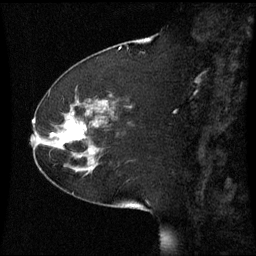
Breast MRI (dynamic contrast-enhanced), one sagittal slice; position 21 of 60 along the scan axis; dynamic contrast-enhanced series, image 2 of 3 at this slice position (ordered by acquisition); 1.5 T; TE 4.2 ms, TR 8.9 ms; 256 × 256 image matrix, field of view 220 × 220 mm. Female patient, age 51 years. From the clinical record (not read from this slice): setting: breast cancer imaged before/during neoadjuvant chemotherapy; receptor status: HR-positive, HER2-negative.
Outlined on this slice (semi-automatic segmentation, software-assisted and operator-edited):
- analysis volume of interest (the breast-tissue region the enhancement analysis was run in; not a lesion): box from (x=44, y=102) to (x=109, y=169) px
- tumour enhancement mask (voxels above the 70 % enhancement threshold inside the analysis volume of interest): (x=52, y=122)–(x=85, y=147)